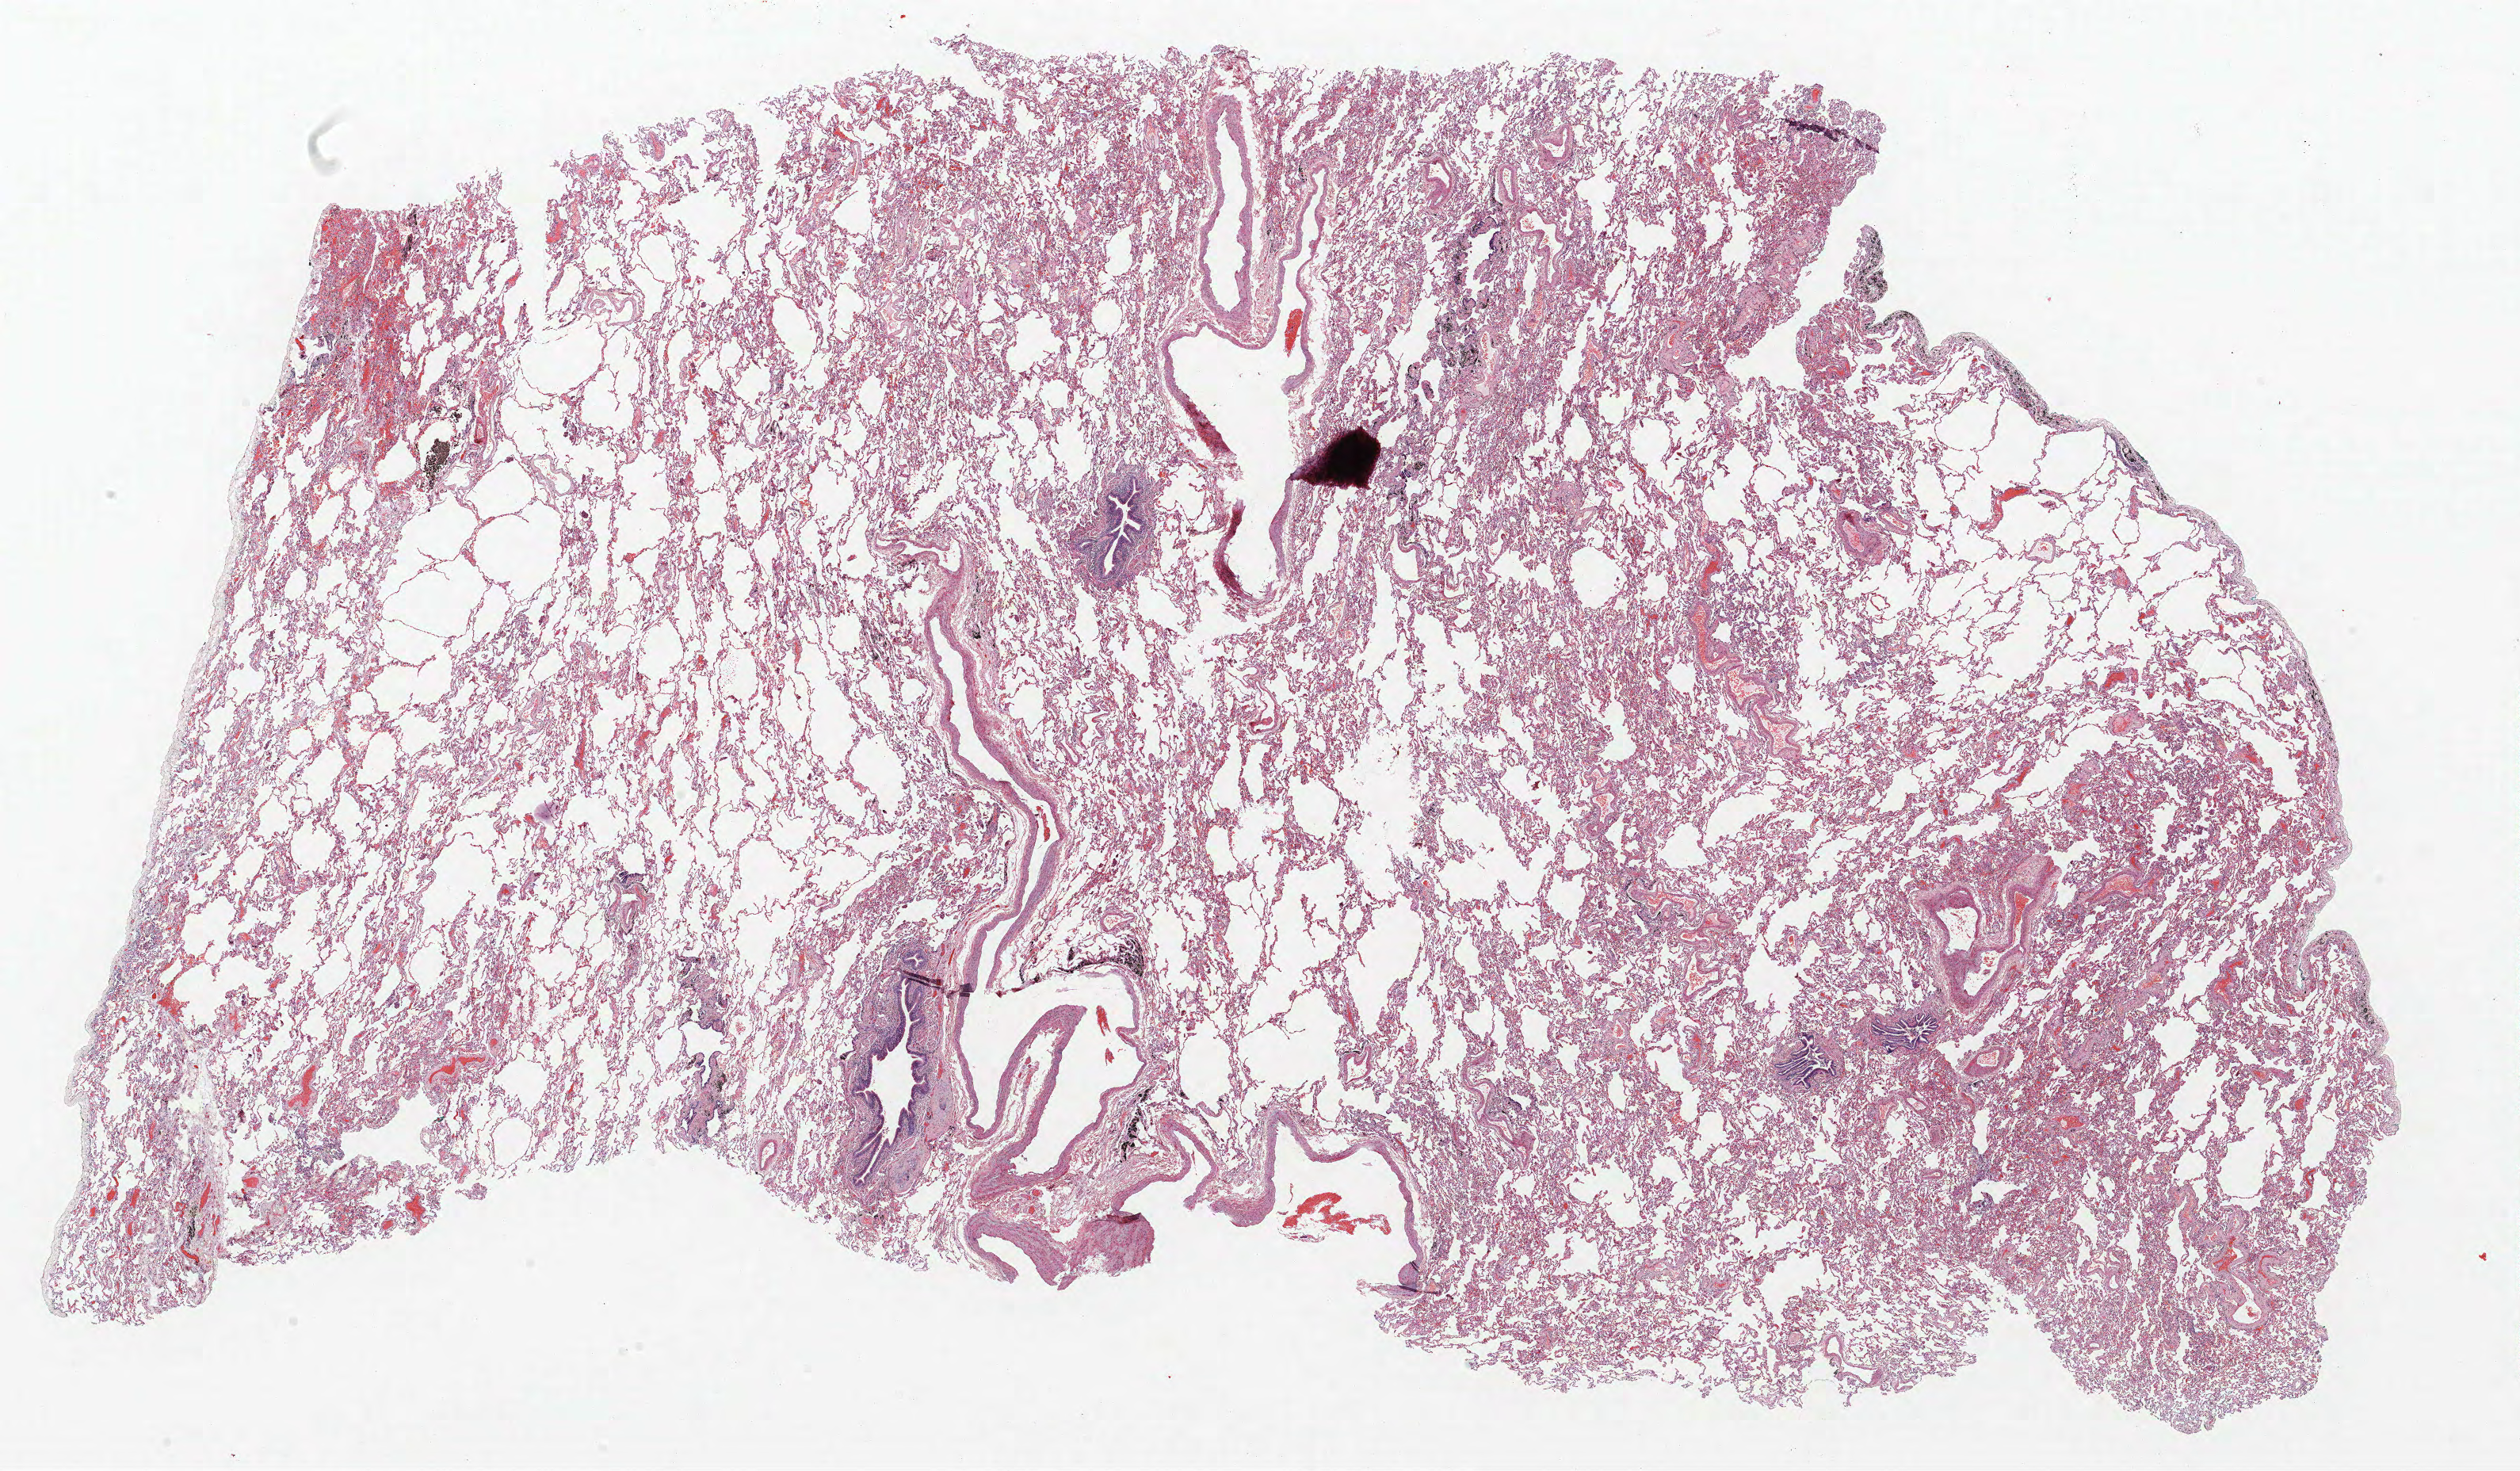
H&E whole-slide image, a low-resolution overview of the entire scanned area, about 25.4 x 14.9 mm (slide scanned at 40x); FFPE section; lung. Male patient, aged 62 at enrolment. Former smoker at enrolment.
Participant's lung-cancer diagnosis: Bronchiolo-alveolar carcinoma, non-mucinous.